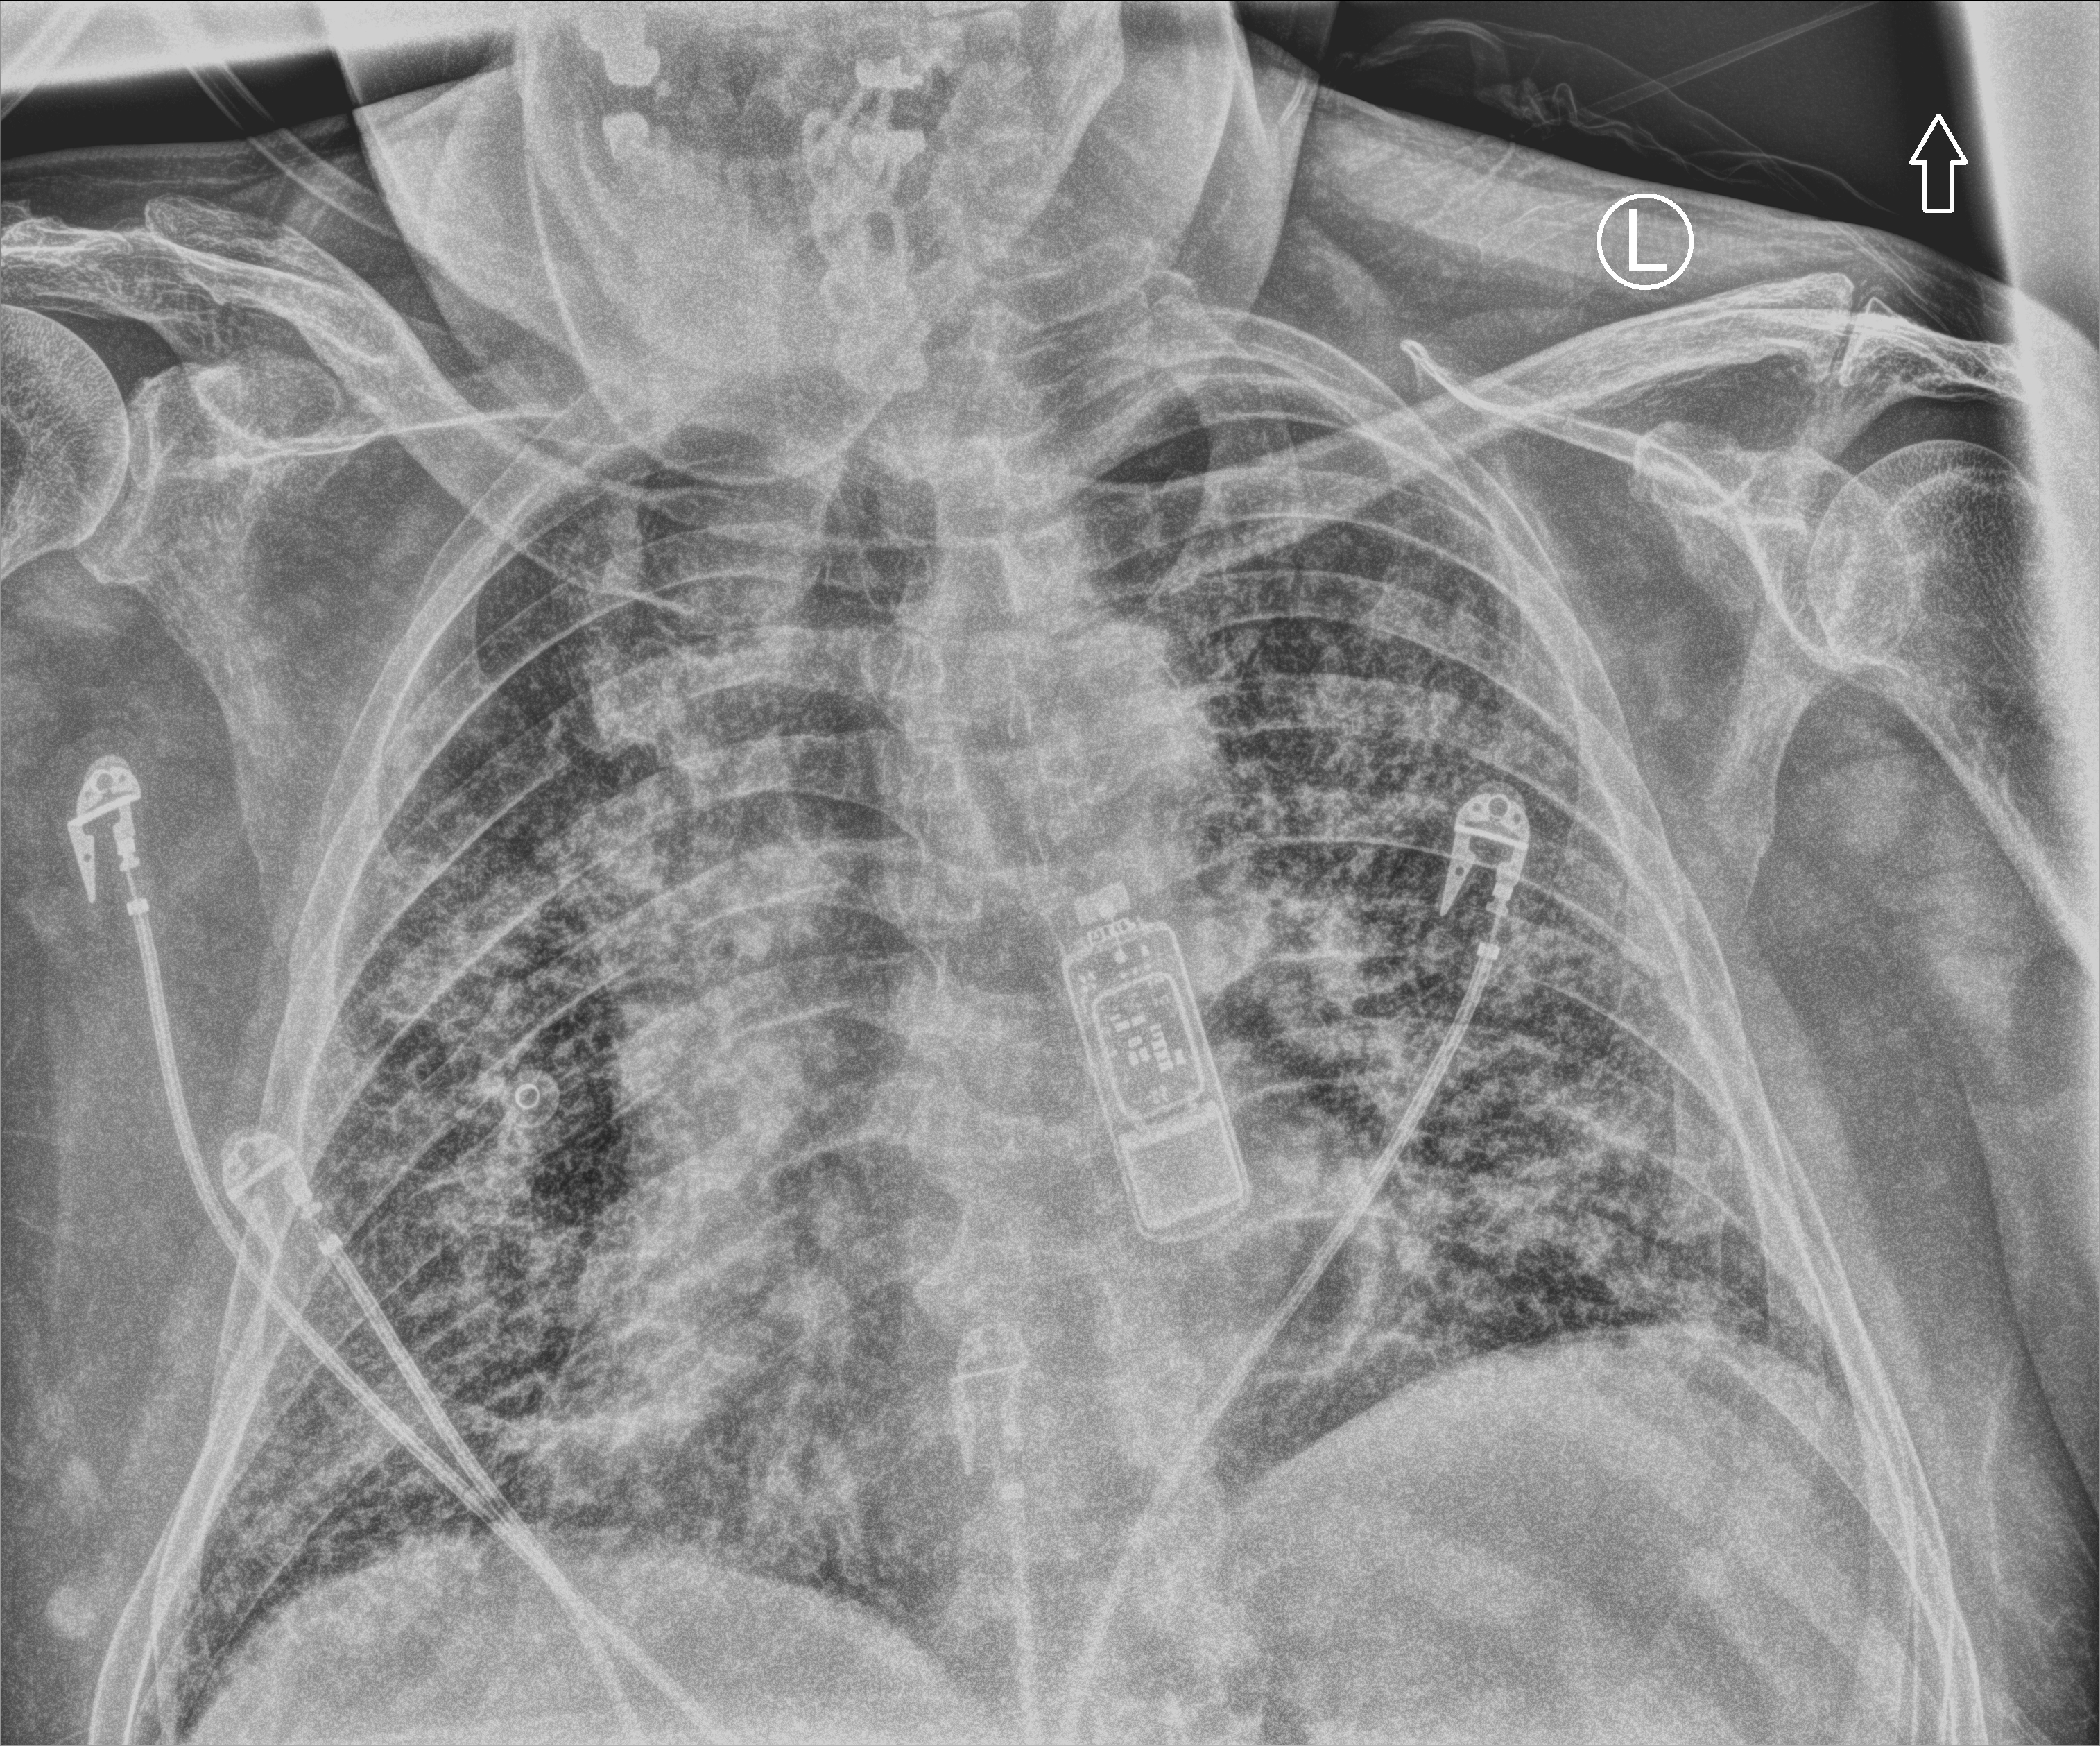
Chest X-ray (portable), anteroposterior (AP) projection. Male patient hospitalised with COVID-19, age 60–74 years.
Admission-level facts for this patient (not findings on this image; timing relative to this image not recorded): admitted to intensive care during this hospital stay: yes.